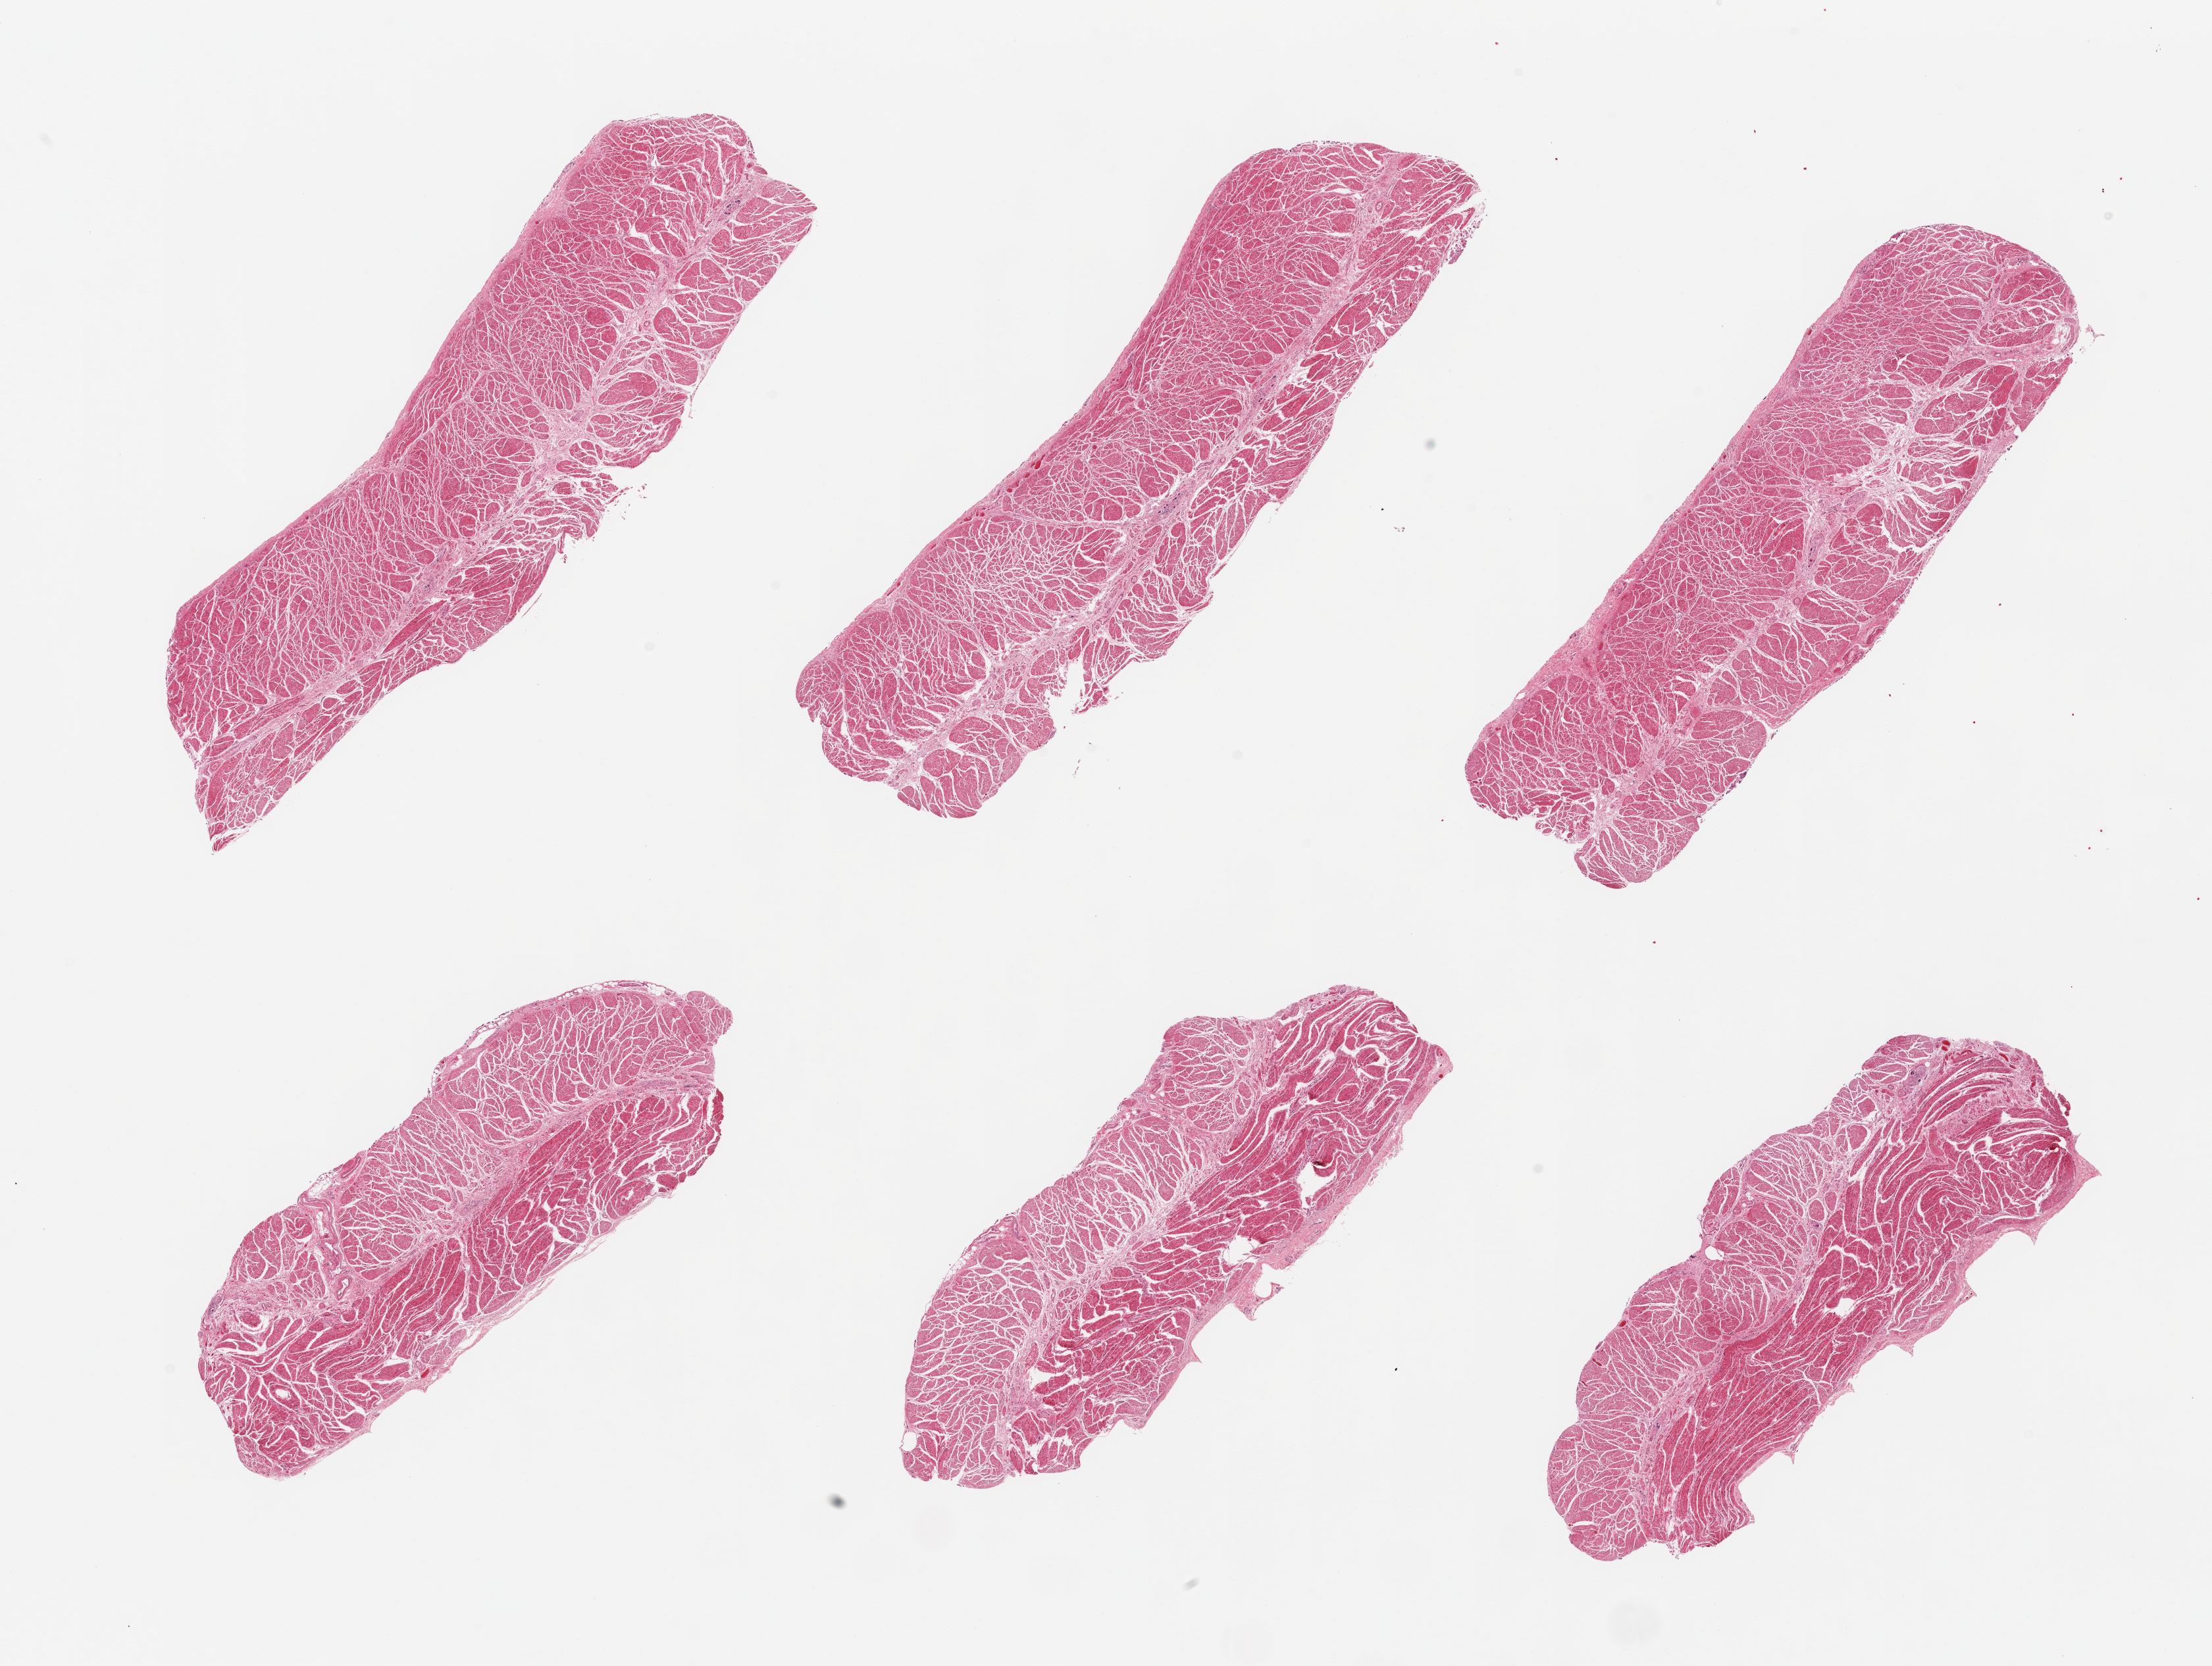
Whole-slide image, hematoxylin and eosin (H&E) stain — low-resolution overview of the scanned area, about 26.6 x 20.0 mm (from a 20x scan), PAXgene-fixed, paraffin-embedded tissue, target tissue: esophageal muscle, tissue donor sample.
- reviewer comment on this tissue sample: 6 pieces, all muscularis